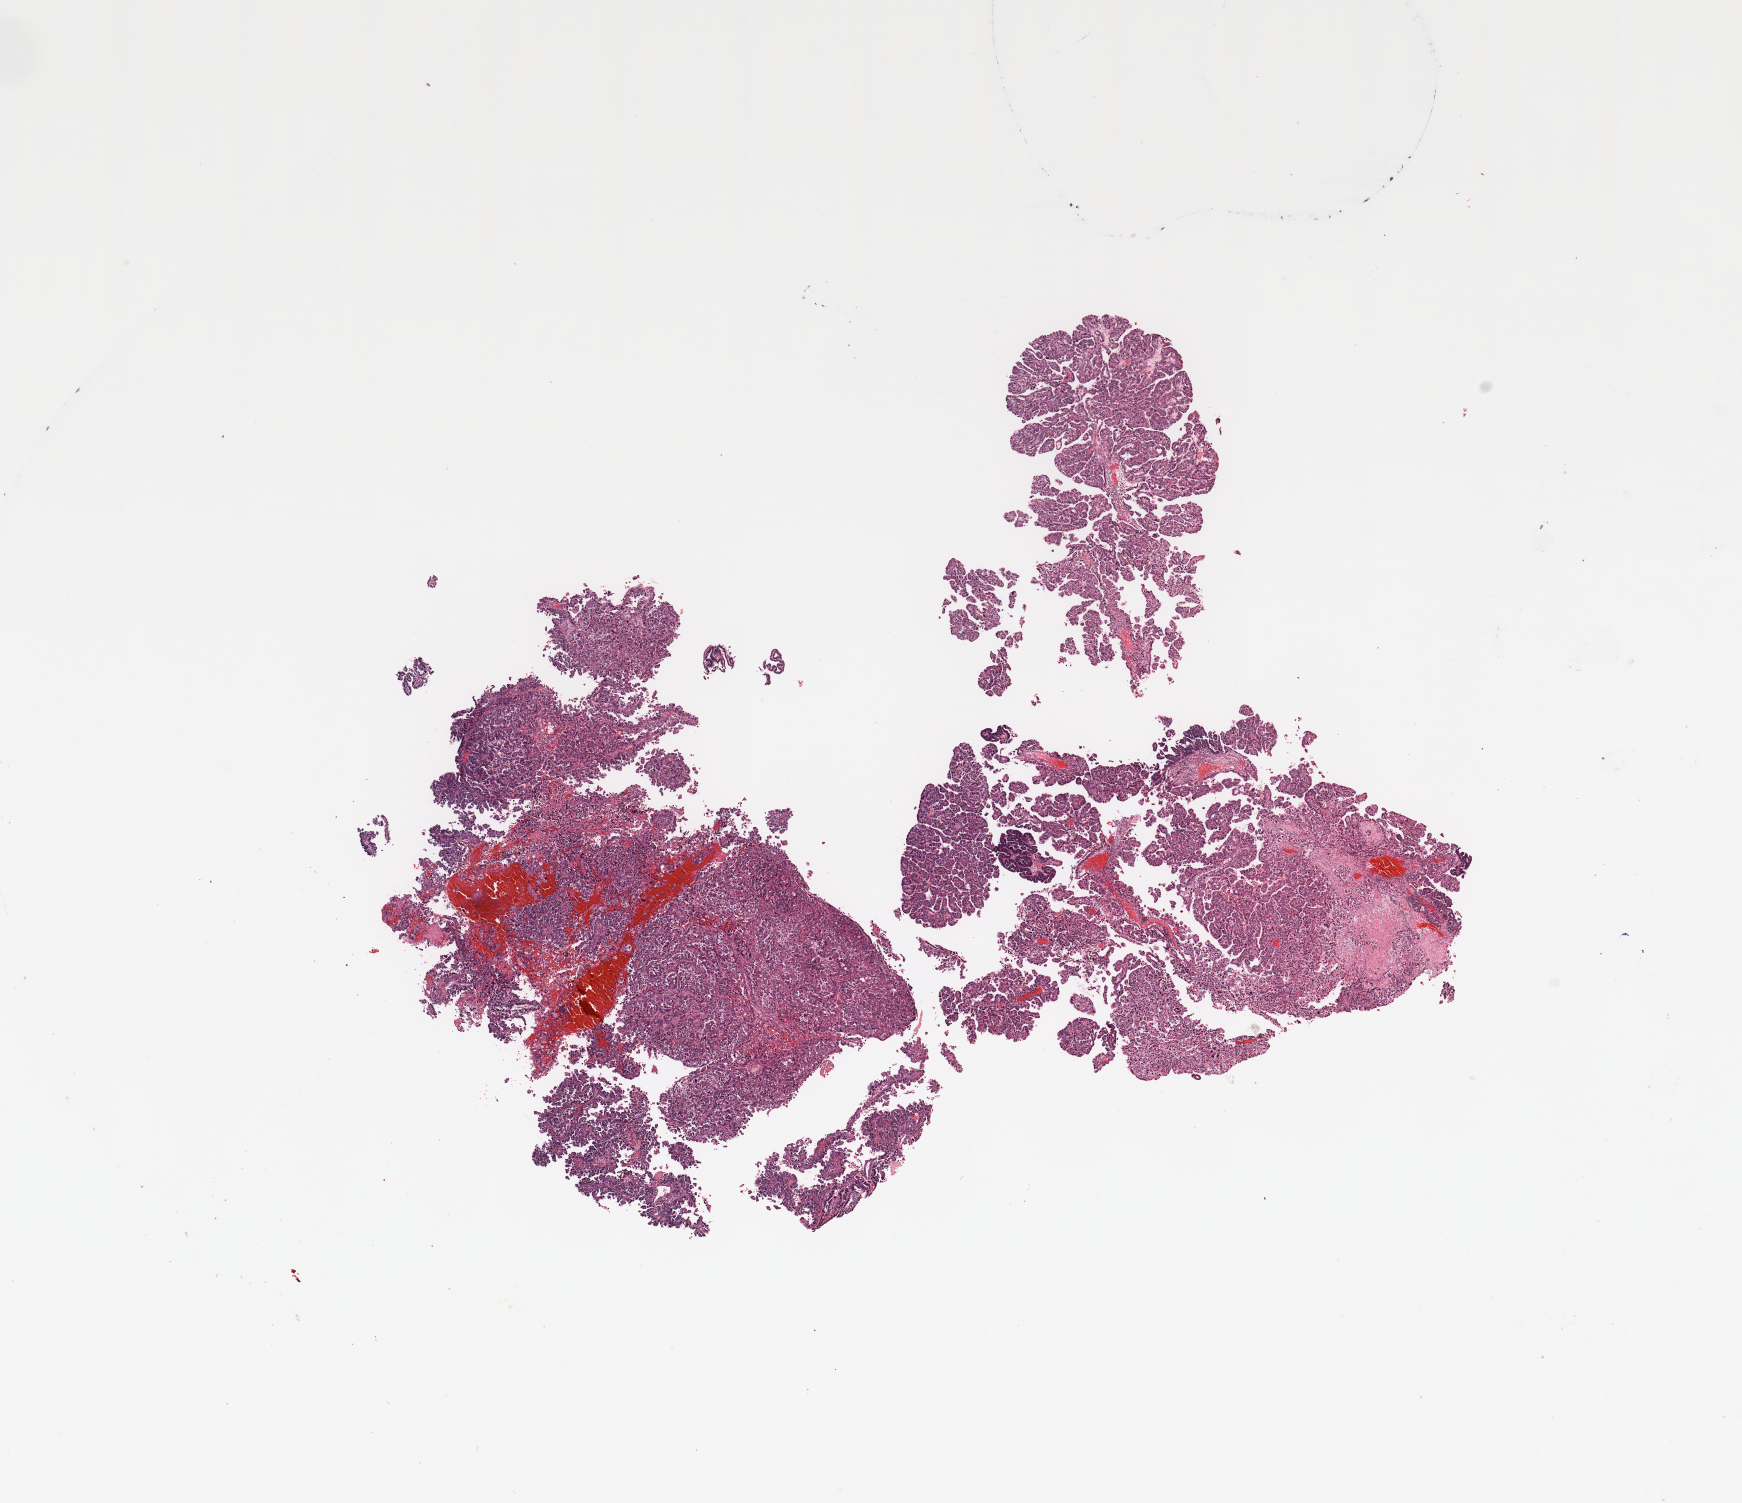
Hematoxylin and eosin (H&E) stained whole-slide image, whole scanned area (about 13.8 x 11.9 mm, from a 20x scan) shown as a low-resolution overview, uterus, tumour tissue. Patient: female, age 69 years.
Patient diagnosis (cohort enrolment): corpus endometrial carcinoma (uterus).